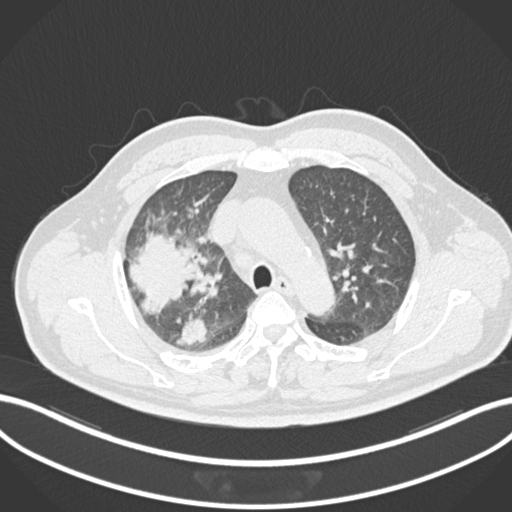
Chest CT, one axial slice; slice 668 of 852 in the series (ordered by position); reconstruction kernel B30f; 120 kVp; lung window (W 1500 / L -600 HU); 512 × 512 image matrix, field of view 400 × 400 mm. Patient: male, 55 years. From the clinical record (not read from this slice): clinical TNM (as recorded): T3 N2 M1.
Outlined on this slice (bounding box drawn by a radiologist):
- lung tumour (recorded histology: adenocarcinoma): bounding box [x1, y1, x2, y2] px = [129, 229, 200, 317]